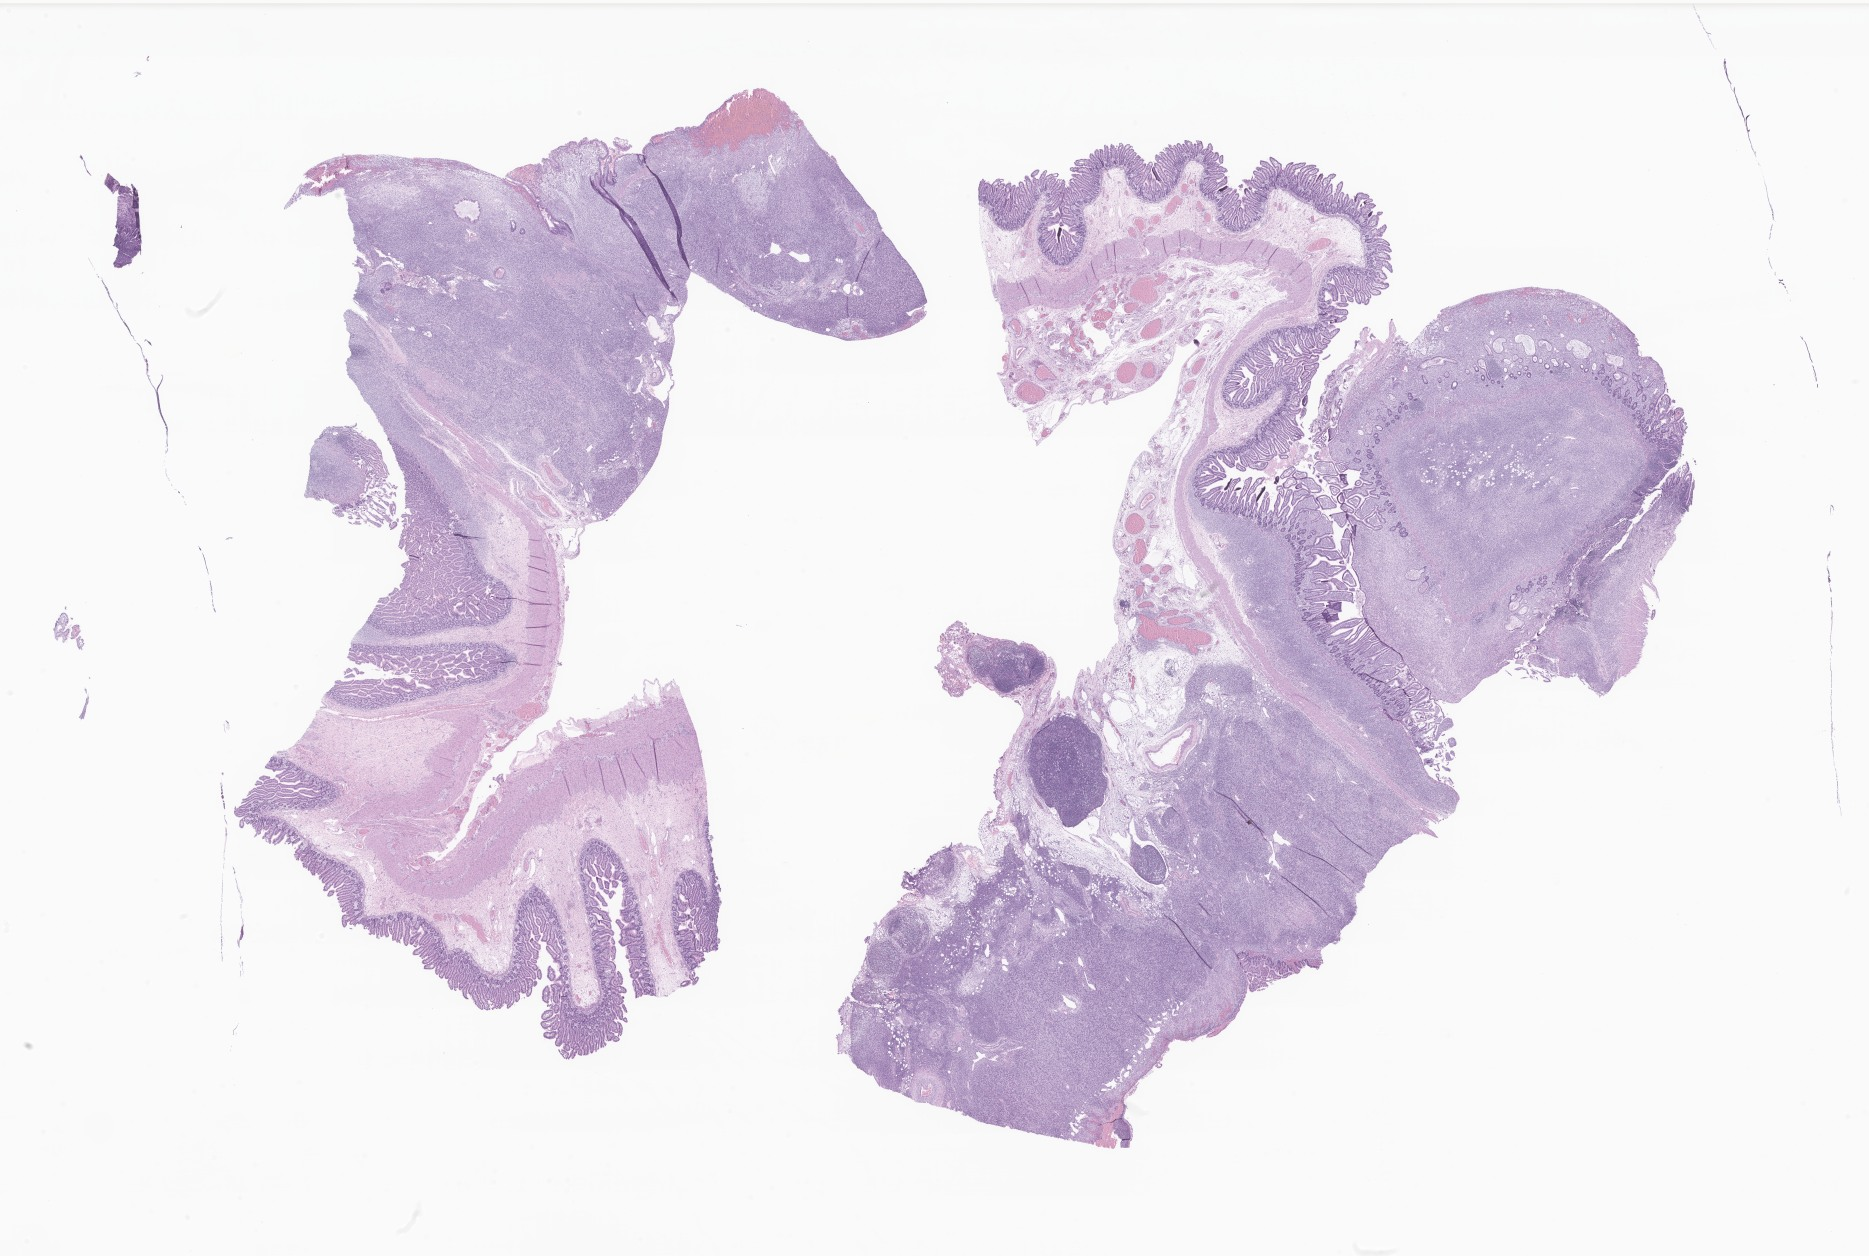
Whole-slide image, hematoxylin and eosin (H&E) stain of tumor tissue from the jejunum — low-resolution overview of the scanned area, about 31.5 x 21.2 mm. FFPE section. Patient female; age 51 days.
Diagnosis (ICD-O-3 morphology term): Infantile fibrosarcoma.